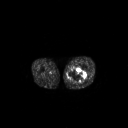
FDG PET of an extremity soft-tissue mass (from a PET/CT study), one axial slice; position 238 of 267 along the scan axis; 3.27 mm slice thickness; 128 × 128 image matrix, field of view 700 × 700 mm. Male patient, age 44 years. From the clinical record (not read from this slice): histological type: undifferentiated pleomorphic liposarcoma; grade: high; site of the primary tumour: left thigh.
Outlined on this slice (expert contour drawn on MRI and transferred to this co-registered scan by the dataset authors):
- gross tumour volume including surrounding oedema: bounding box (x1, y1, x2, y2) in pixels: (67, 68, 86, 83)
- gross tumour volume (mass): (67, 68, 86, 83)